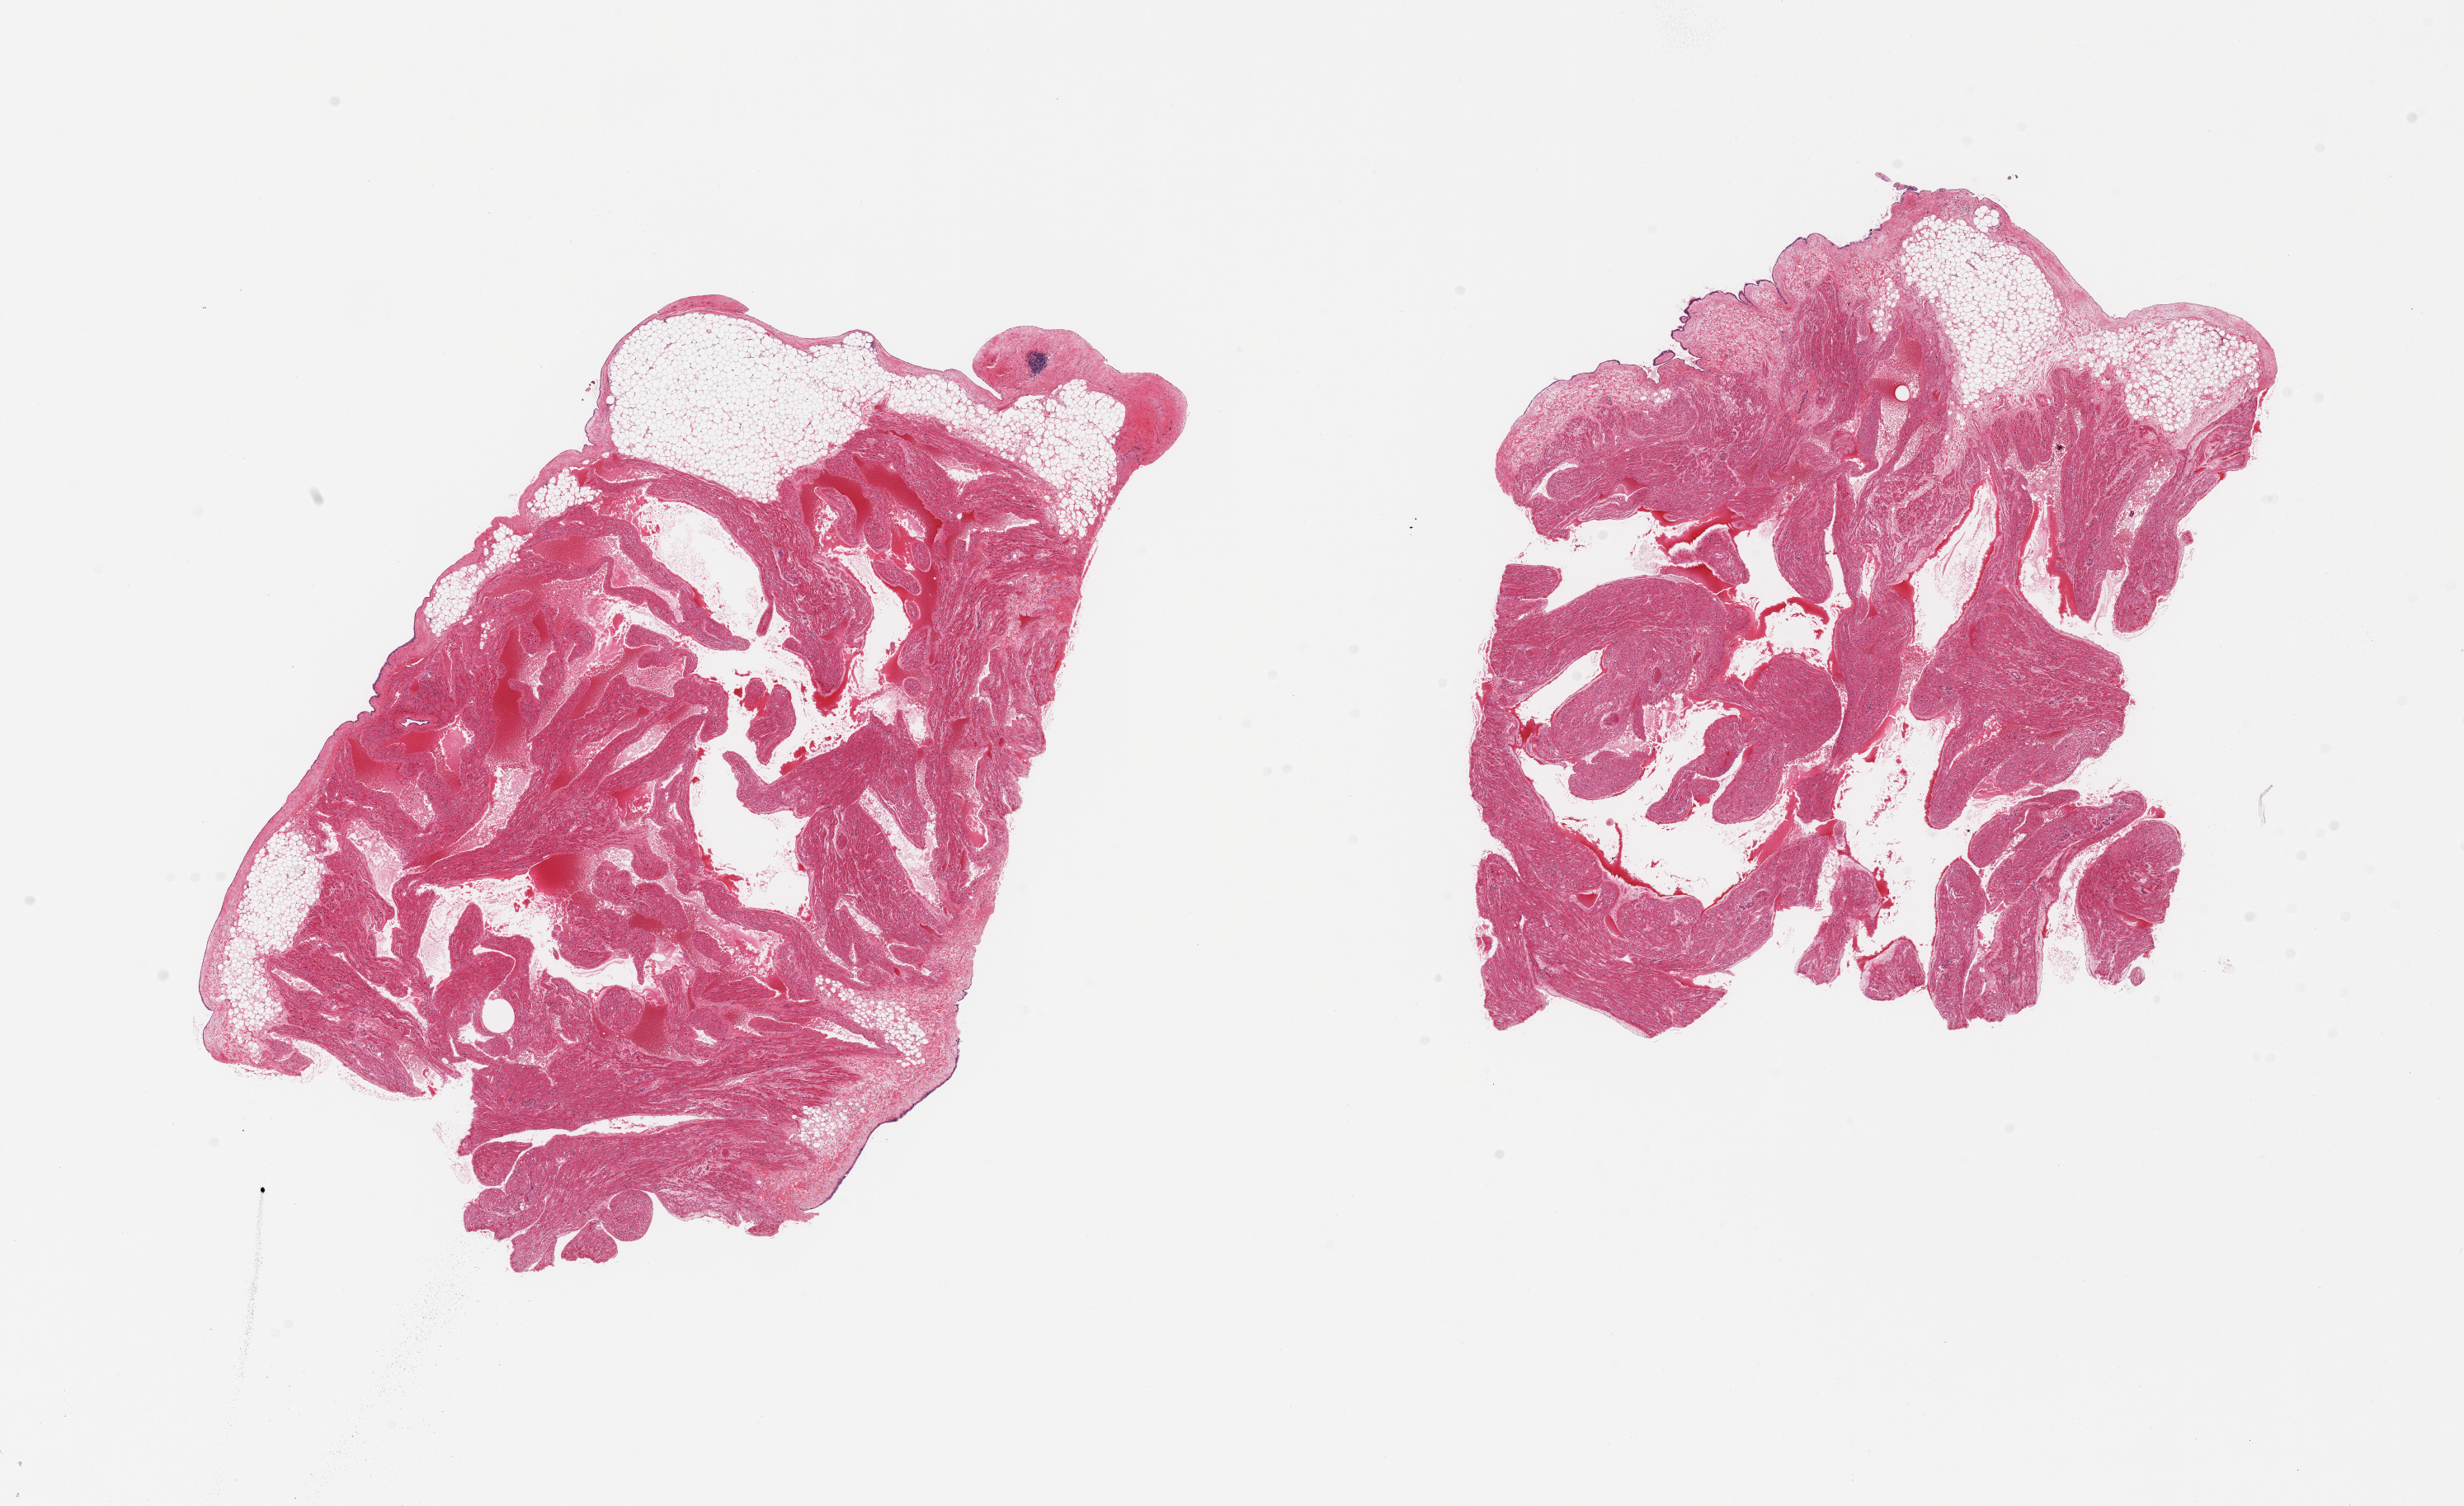
Digitized haematoxylin and eosin-stained section — whole scanned area (about 23.6 x 14.4 mm) shown as a low-resolution overview, PAXgene-fixed paraffin-embedded (PFPE) section, sampled site (target tissue): auricular appendage, donor tissue sample. Donor sex: male.
Pathologist's review note for this sample: 2 pieces, no abnormalities.